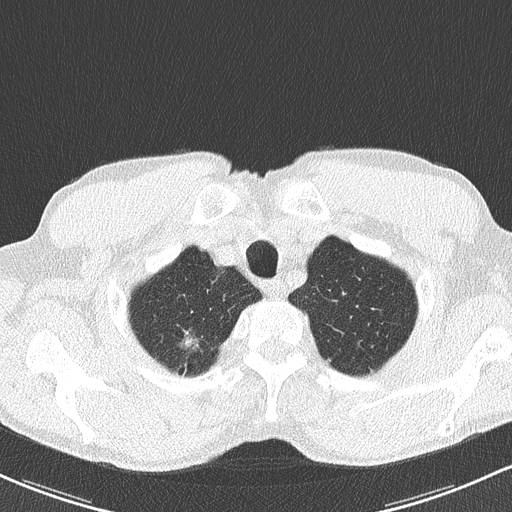
Chest CT (low-dose screening protocol), one axial image. Baseline annual screen. Lung window (W 1500 / L -600 HU). 2 mm slice thickness. Lung (sharp) reconstruction kernel (B50f). 512 × 512 image matrix. Male participant, aged 62 years at enrolment. Former smoker at enrolment.
• Expert-annotated lung lesion, bounding box [x1, y1, x2, y2] px = [165, 326, 210, 367].
• Reader record for this screening exam (exam-level; its link to the box is not recorded): non-calcified nodule or mass ≥4 mm, right upper lobe, 12 × 9 mm, spiculated (stellate) margins, soft tissue attenuation.
• Official screen result: positive, change unspecified: nodule(s) >= 4 mm or enlarging nodule(s), mass(es), or other non-specific abnormalities suspicious for lung cancer.
• Participant outcome: lung cancer diagnosed 398 days after this screen — bronchiolo-alveolar adenocarcinoma, NOS, right upper lobe, well differentiated (G1), stage IA (AJCC 6th edition), 15 mm at pathology.